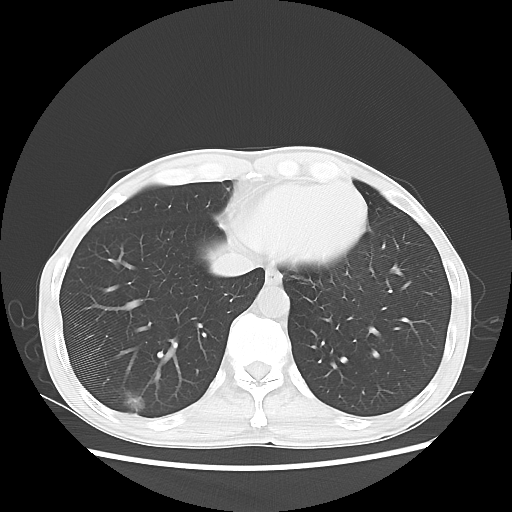
Chest CT, one axial slice. Slice 19 of 68 in the series (ordered by position). 100 kVp. Lung window (W 1500 / L -600 HU). 5 mm slice thickness. 512 × 512 image matrix. Male patient, age 60 years. Case-level facts recorded for this patient, not image findings: clinical TNM (as recorded): T1c N0 M0; histopathological grade: G2.
Structures marked on this image (bounding box drawn by a radiologist):
- lung tumour (recorded histology: adenocarcinoma): bounding box (x1, y1, x2, y2) in pixels: (116, 389, 157, 420)